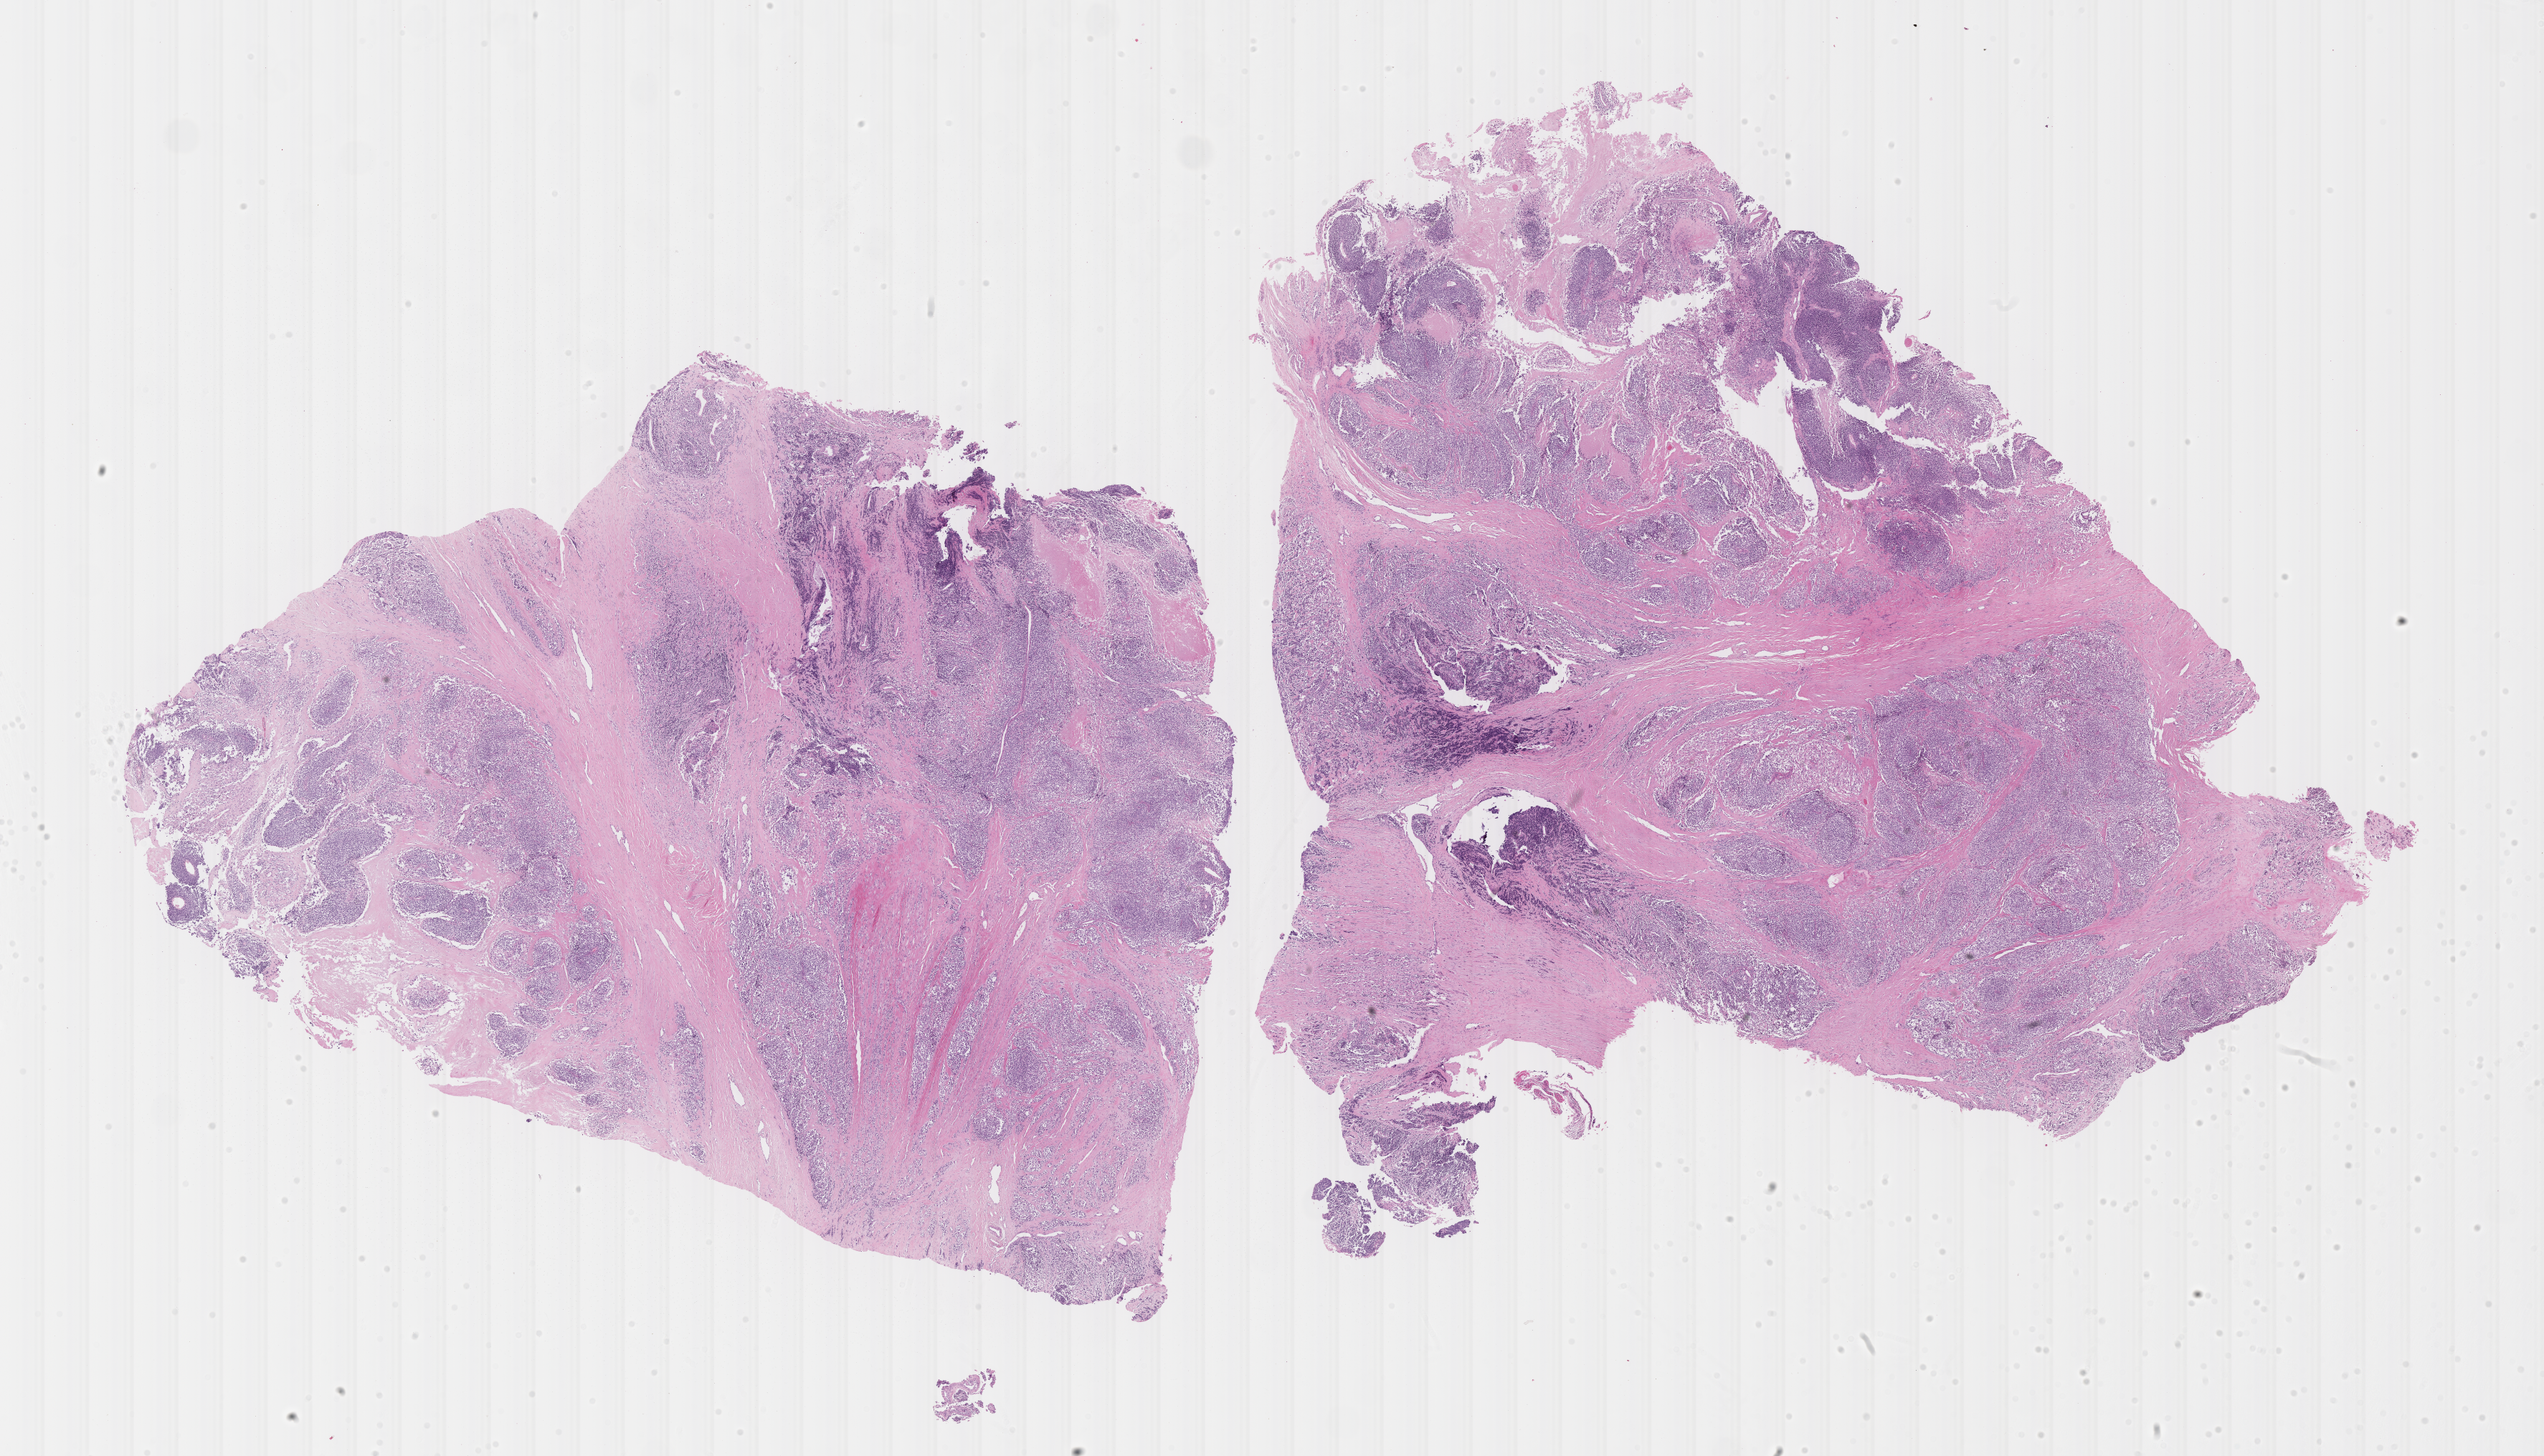
Hematoxylin and eosin (H&E) whole-slide image of tumor tissue — low-resolution overview of the scanned area, about 28.7 x 16.4 mm, formalin-fixed, paraffin-embedded (FFPE) tissue. Female patient, age at diagnosis 8.6 years.
Diagnosis: rhabdomyosarcoma; histological classification: alveolar rhabdomyosarcoma.